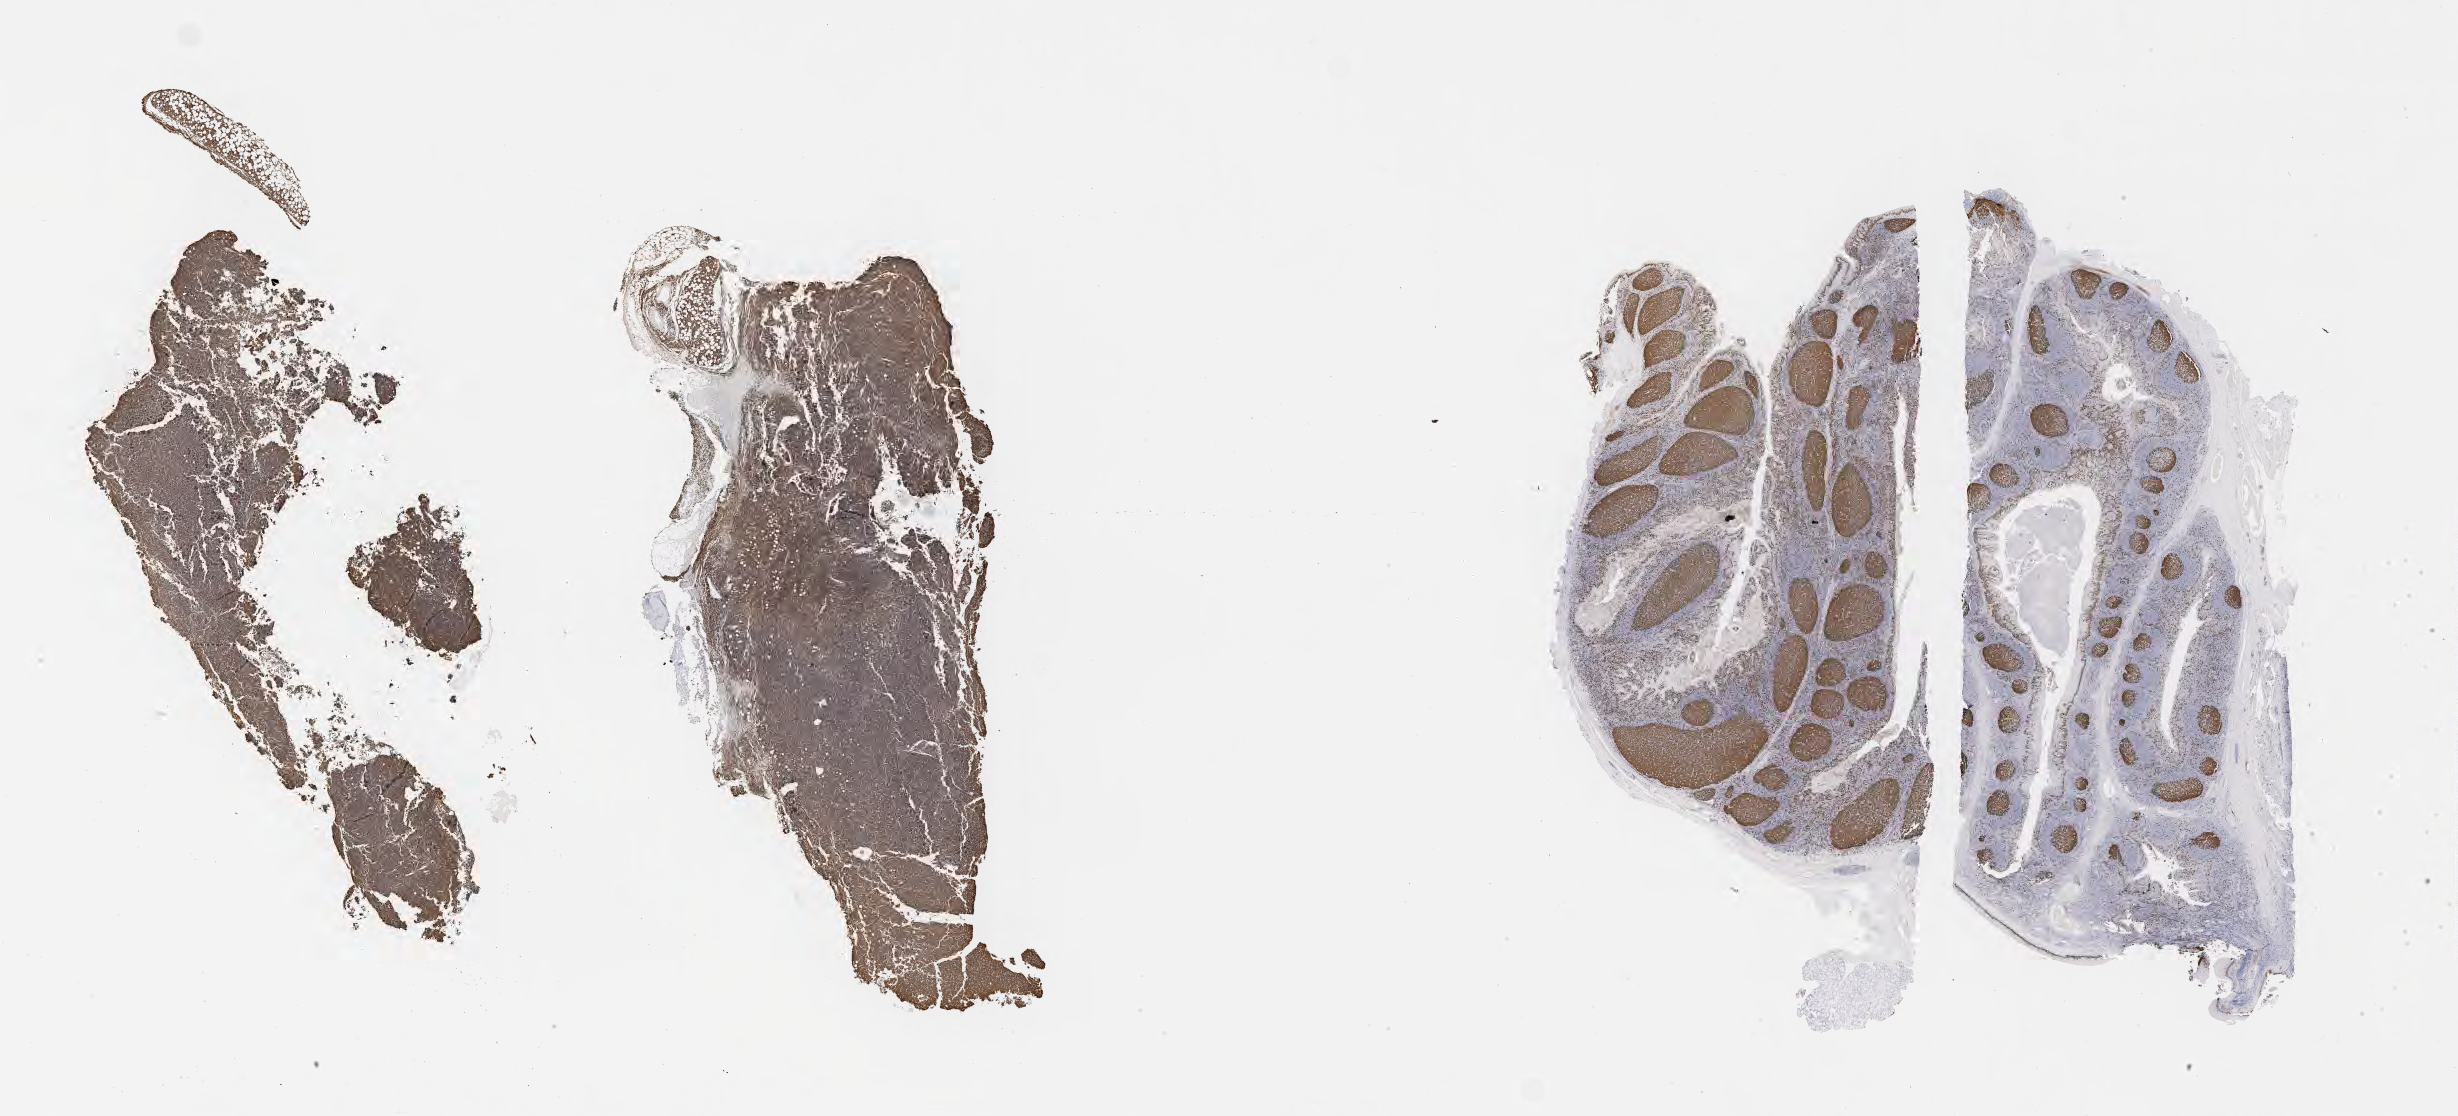
Immunohistochemistry (IHC) whole-slide image stained for Ki-67, a low-resolution overview of the entire scanned area, about 39.8 x 18.0 mm. Tumor tissue. Patient female; age 16 years.
* diagnosis: Burkitt lymphoma, NOS